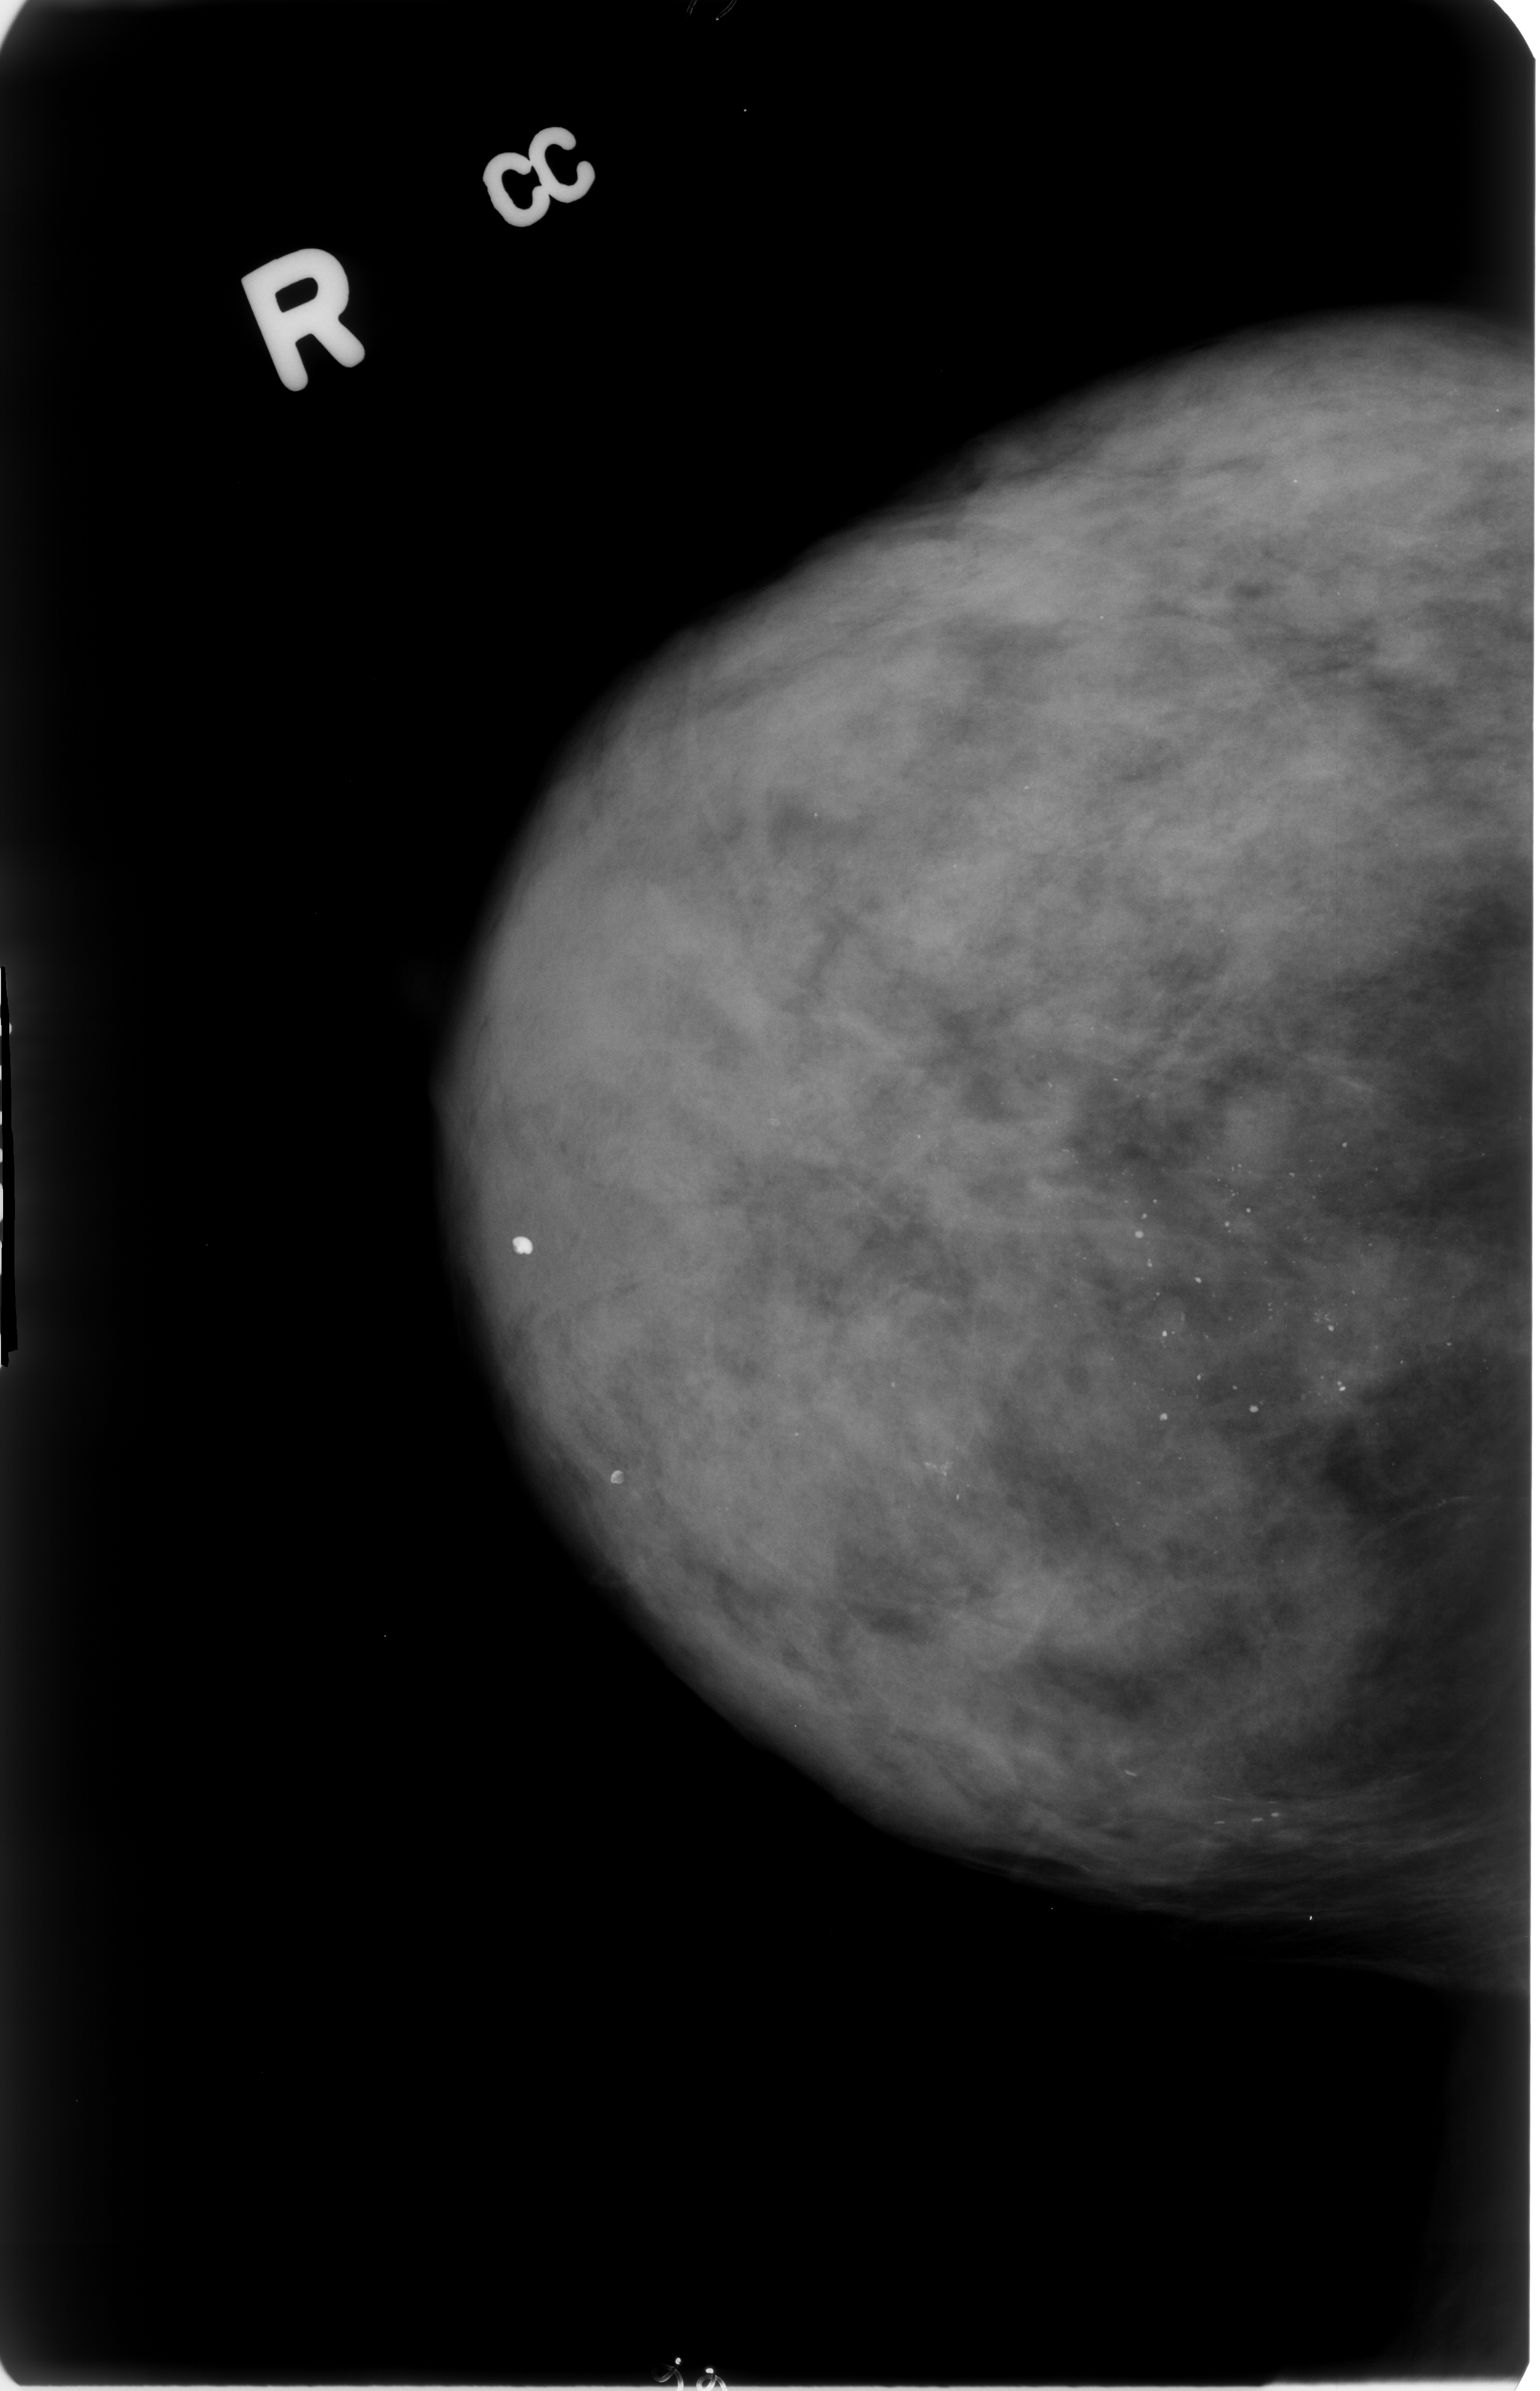
Digitized screen-film mammogram. Right breast. Craniocaudal (CC) view. Breast composition: extremely dense (BI-RADS density category 4 of 4). 1540 × 2391 image matrix.
Expert-marked regions of interest on this film, with their recorded descriptors:
- calcifications, morphology vascular / coarse / lucent center / round and regular / punctate, distribution regional; BI-RADS assessment category 2; subtlety rating 5 on a 1 (subtle) to 5 (obvious) scale; benign; no additional work-up was recommended (outcome (as recorded, no biopsy): benign without callback): bounding box <1118,1181,1368,1434> (left, top, right, bottom; pixels)